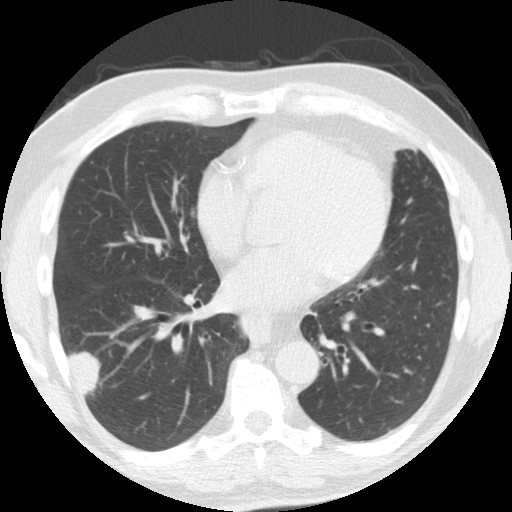
Low-dose screening chest CT, one axial slice; slice 75 of 174 in the series (ordered by position); reconstruction kernel STANDARD; 120 kVp; lung window (W 1500 / L -600 HU); 2.5 mm slice thickness; 512 × 512 image matrix, field of view 341 × 341 mm.
Annotated regions visible in this slice (outlined manually by an expert reader):
- lesion 1 (tumor, lower lobe of right lung): bounding box [x1, y1, x2, y2] px = [69, 352, 100, 394]